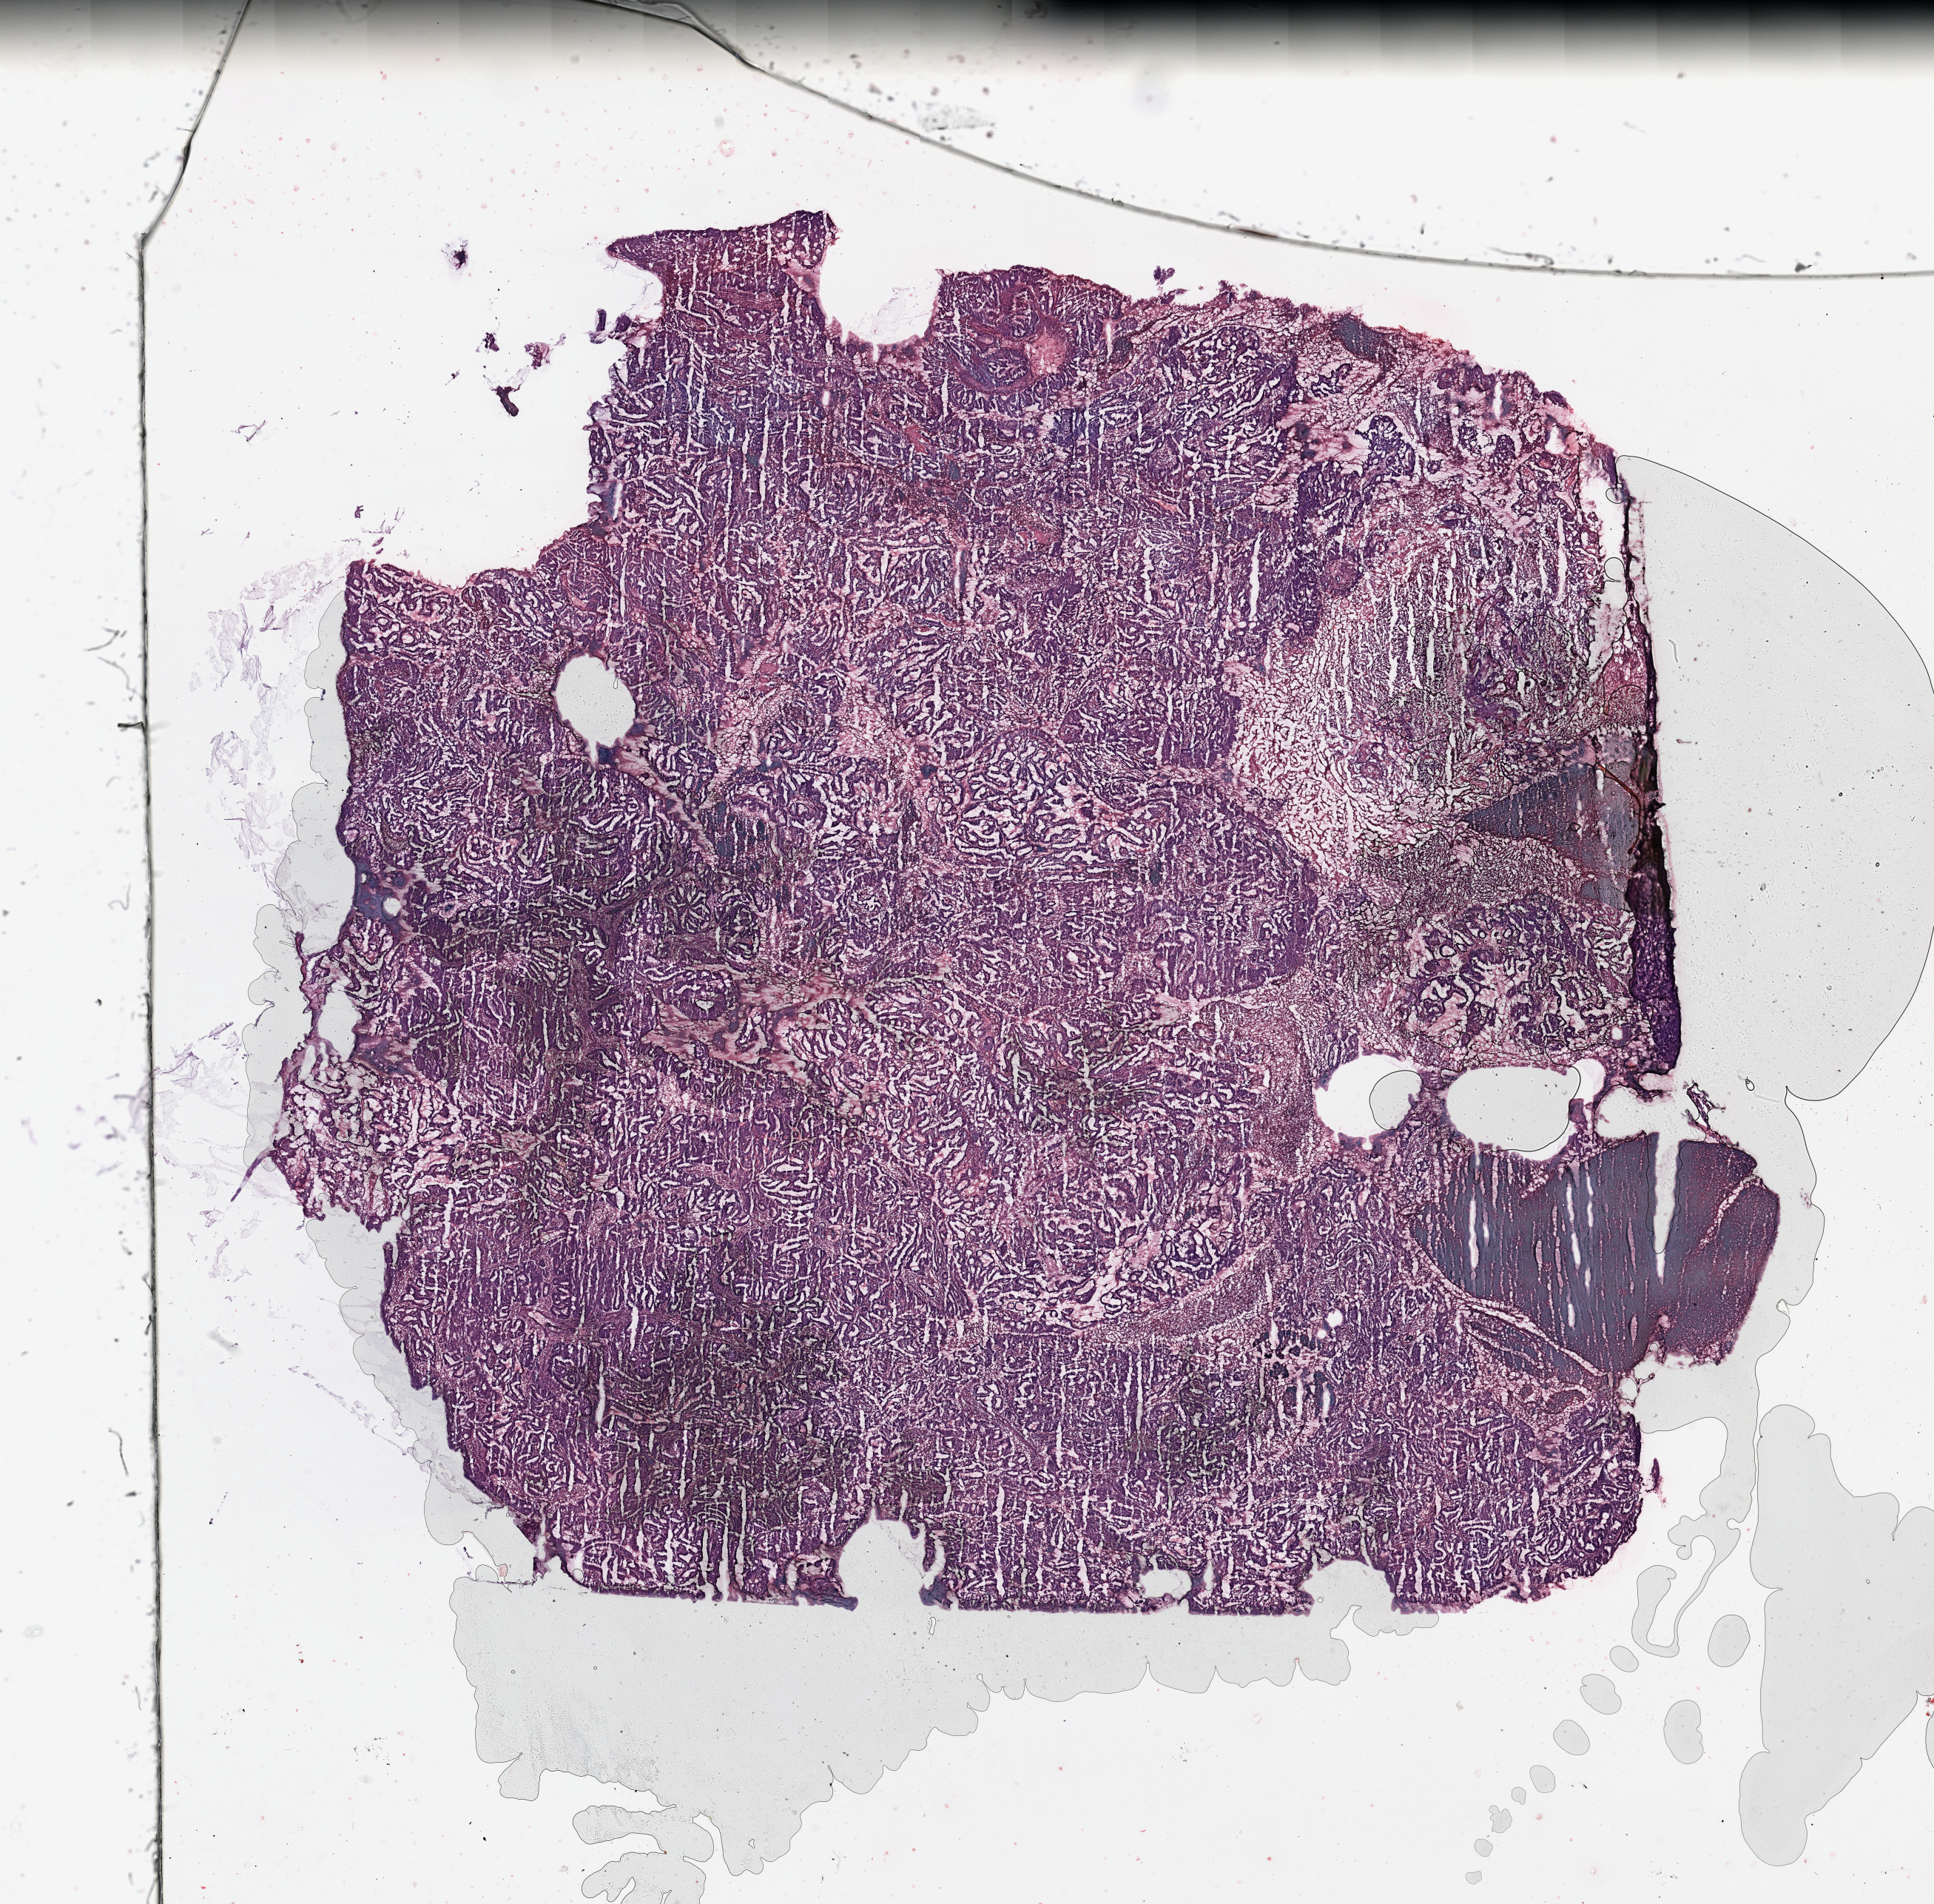
H&E-stained whole-slide image — low-resolution overview of the scanned area, about 20.7 x 20.3 mm. Tumour tissue sample, uterus. Patient: female, age 64 years. Histologic grade: G2 (moderately differentiated).
* histologic diagnosis: Endometrioid adenocarcinoma, NOS
* AJCC pathologic stage: I